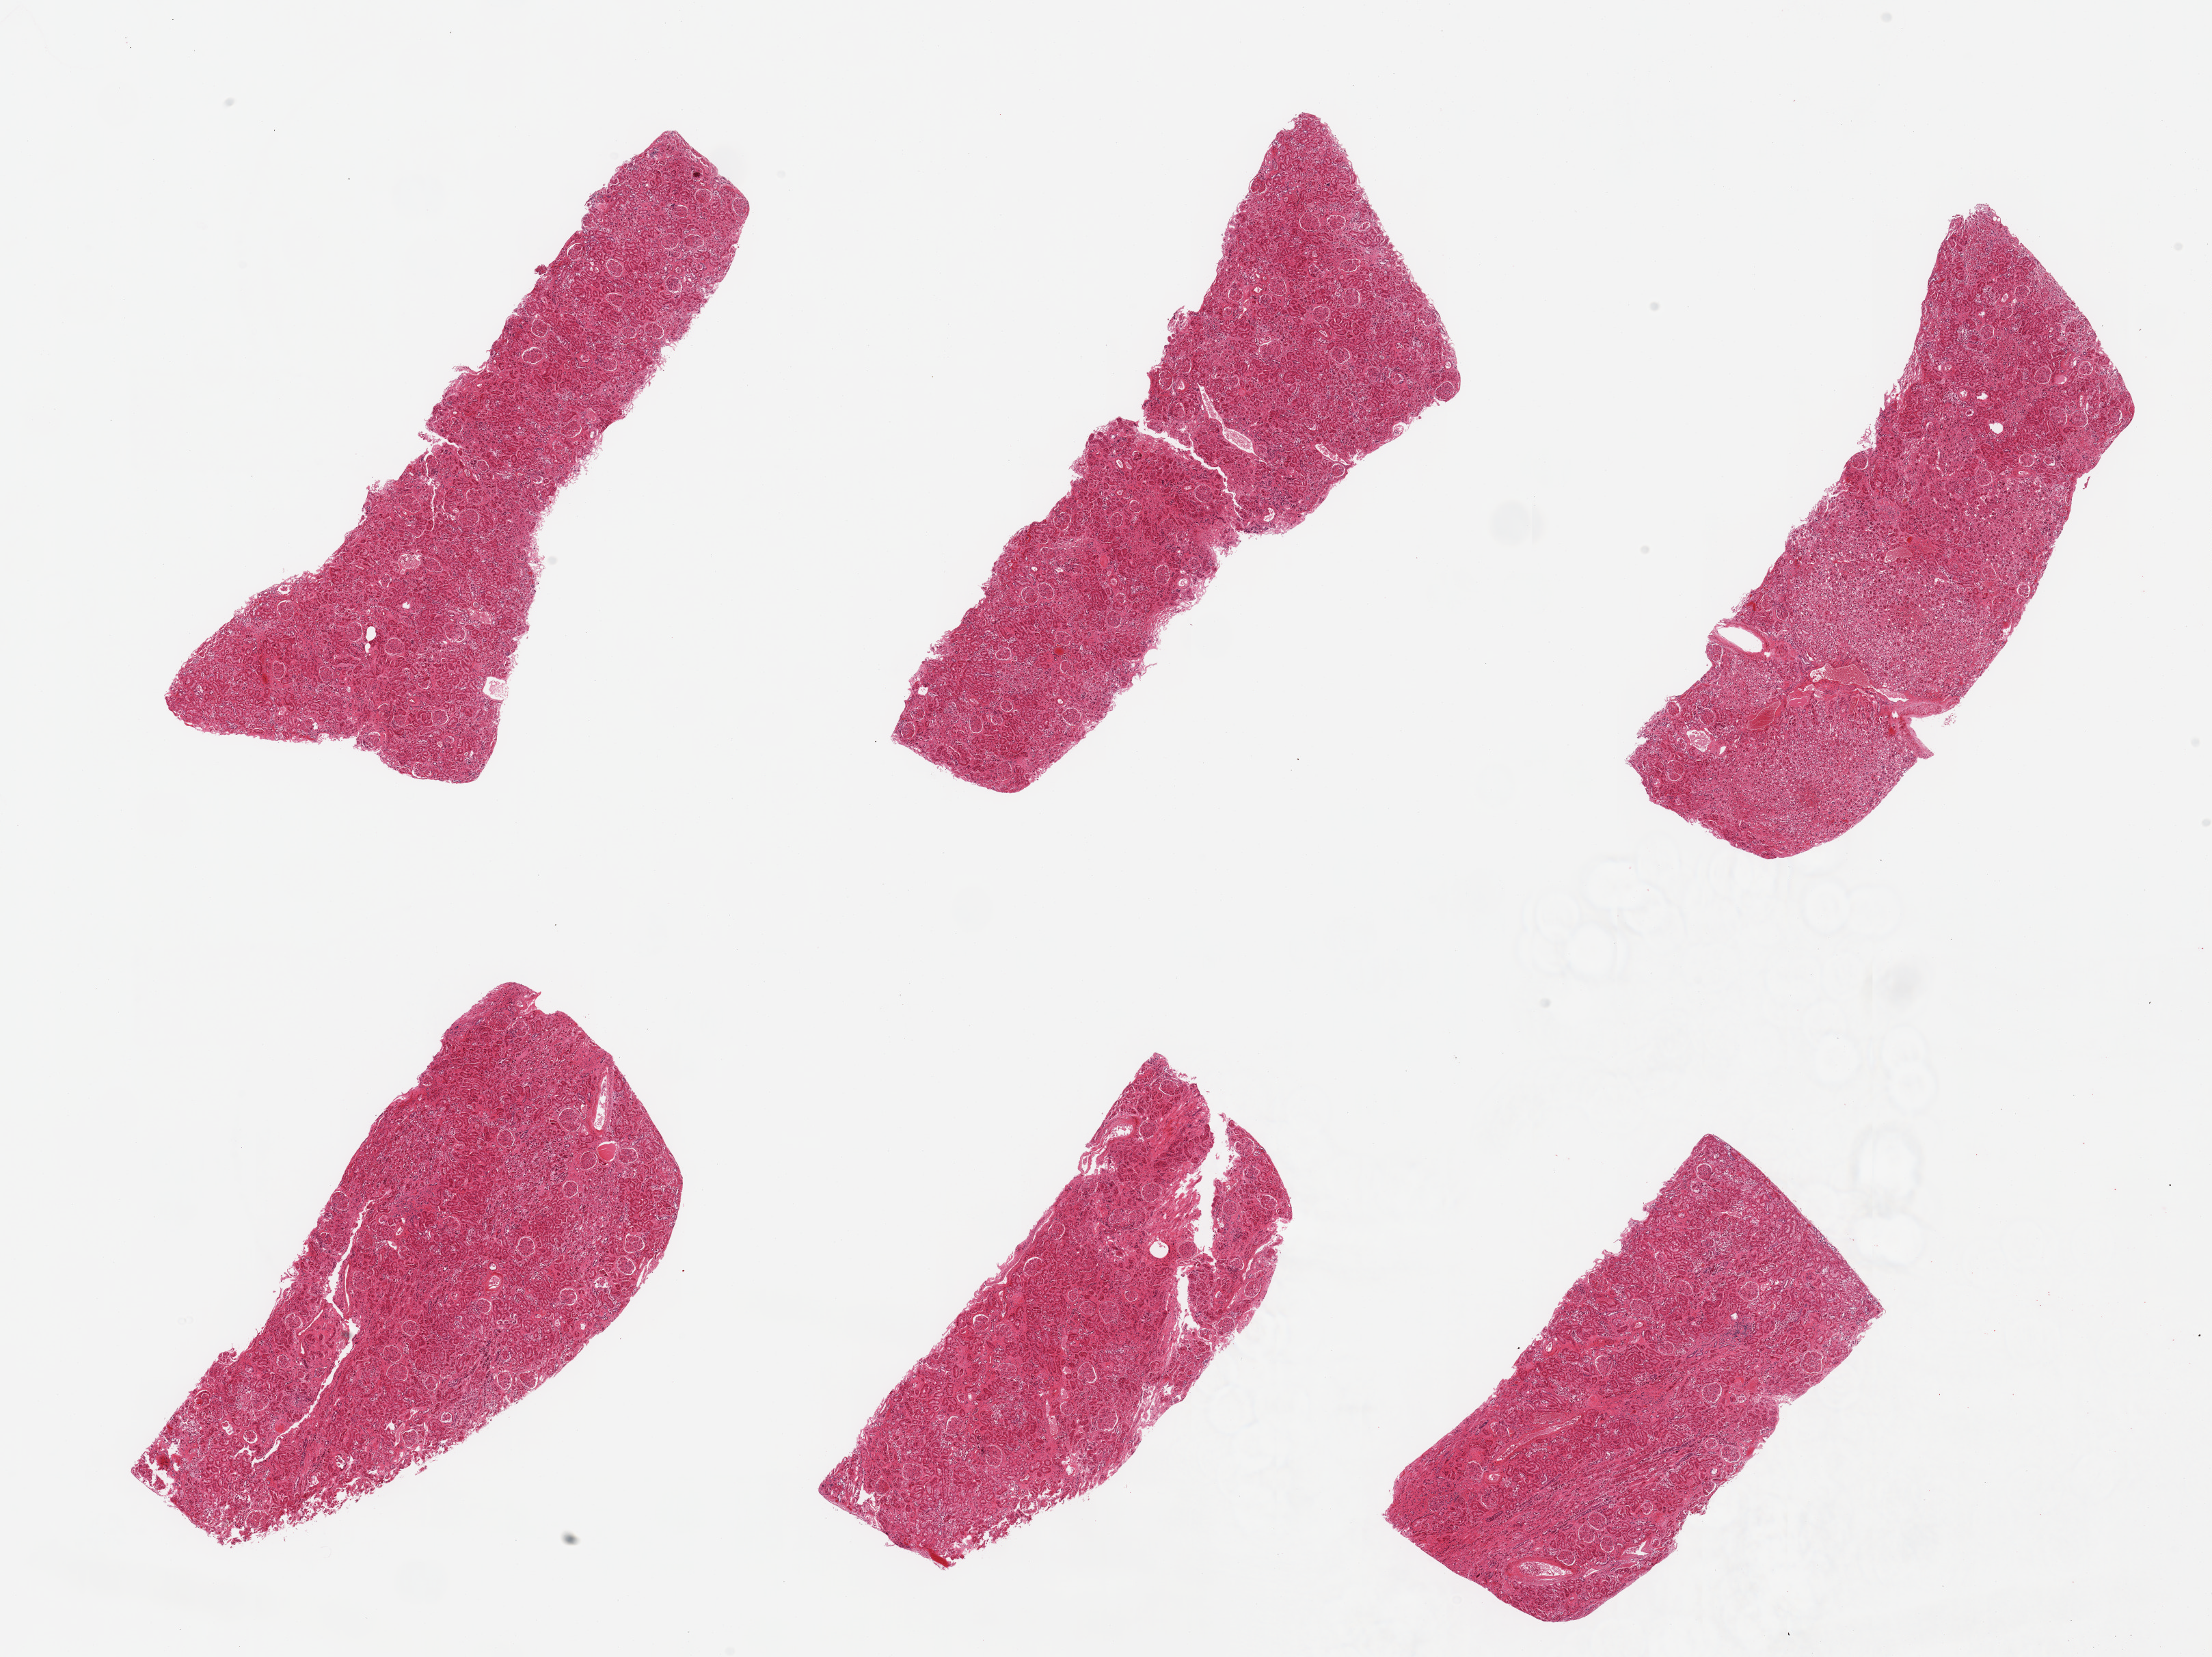
Whole-slide image, haematoxylin and eosin stain — low-resolution overview of the scanned area, about 25.6 x 19.2 mm. PAXgene-fixed paraffin-embedded (PFPE) section. Section of renal cortex (target tissue). Donor tissue sample. Male donor.
Review note (as recorded): 6 pieces; glomeruli in all sections.